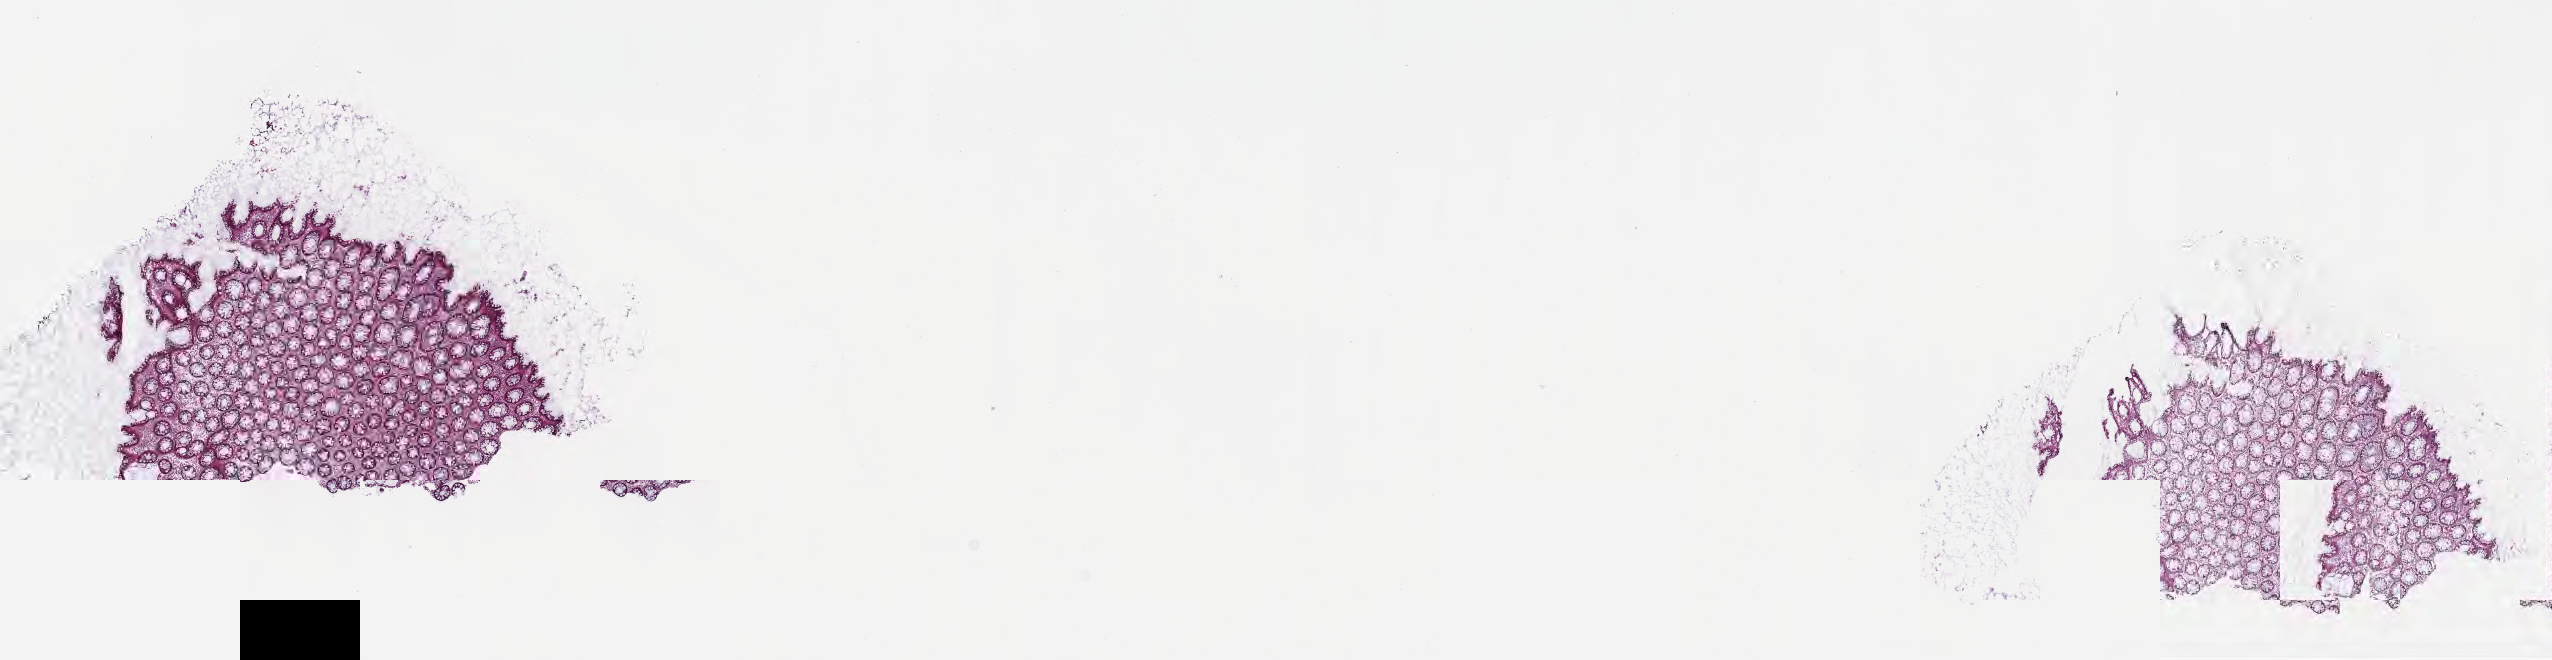
Digitized hematoxylin and eosin (H&E)-stained section — shown as a low-resolution overview of the whole scanned area (about 20.6 x 5.3 mm); frozen section (tissue freezing medium); specimen: metastatic tumor tissue, resected from liver. Male patient; age at initial diagnosis 72 years. Pathologist review of this section (percent, as recorded): tumor cells 0%, tumor nuclei 0%, stromal cells 30%, necrosis 0%, normal cells 70%. Inflammatory infiltration, as recorded: lymphocyte infiltration 7%, monocyte infiltration 4%, neutrophil infiltration 8%.
Patient diagnosis (primary): Adenocarcinoma, NOS.